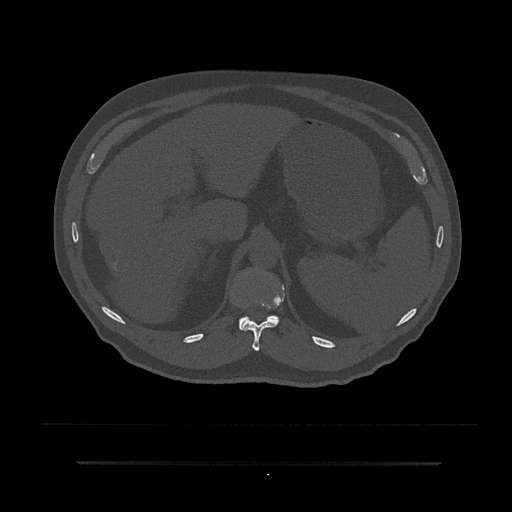
CT including the spine, one axial slice. Position 245 of 797 along the scan axis. Reconstruction kernel Br40s/3. Bone window (W 1800 / L 400 HU). 0.5 mm slice thickness. 512 × 512 image matrix, field of view 464 × 464 mm. Patient: male, 59 years. Case-level facts recorded for this patient, not image findings: primary cancer: bile ducts.
Annotated regions visible in this slice (semi-automatic segmentation, software-assisted and operator-edited):
- T11 vertebra: box from (x=242, y=295) to (x=283, y=351) px
- T12 vertebra: (x=239, y=315)–(x=279, y=331)